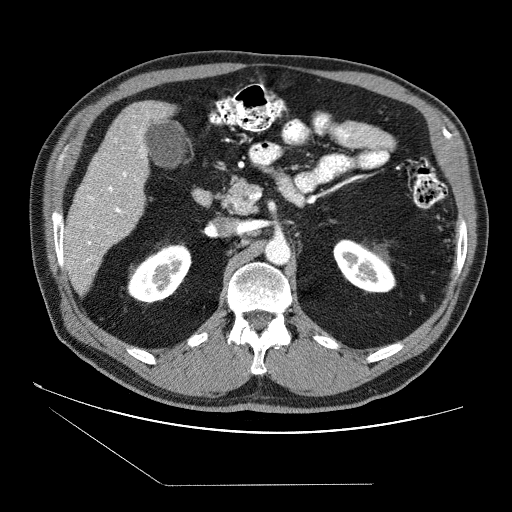
Contrast-enhanced abdominal CT (liver protocol), one axial slice. Reconstruction kernel STANDARD. 120 kVp. Soft-tissue window (W 400 / L 40 HU). 2.5 mm slice thickness. 512 × 512 image matrix. Case-level facts recorded for this patient, not image findings: diagnosis: hepatocellular carcinoma (patient treated with transarterial chemoembolisation; whether this scan precedes or follows treatment is not stated here); TNM stage (as recorded): Stage-II; Child-Pugh class: B; tumour differentiation: no biopsy; tumour nodularity: multinodular.
Annotated regions visible in this slice (semi-automatic segmentation, software-assisted and operator-edited):
- liver parenchyma outside the tumour (the mass and vessels are separate outlines, so this box may not span the whole liver): bounding box [x1, y1, x2, y2] px = [64, 100, 172, 294]
- liver vessels: [73, 126, 145, 261]